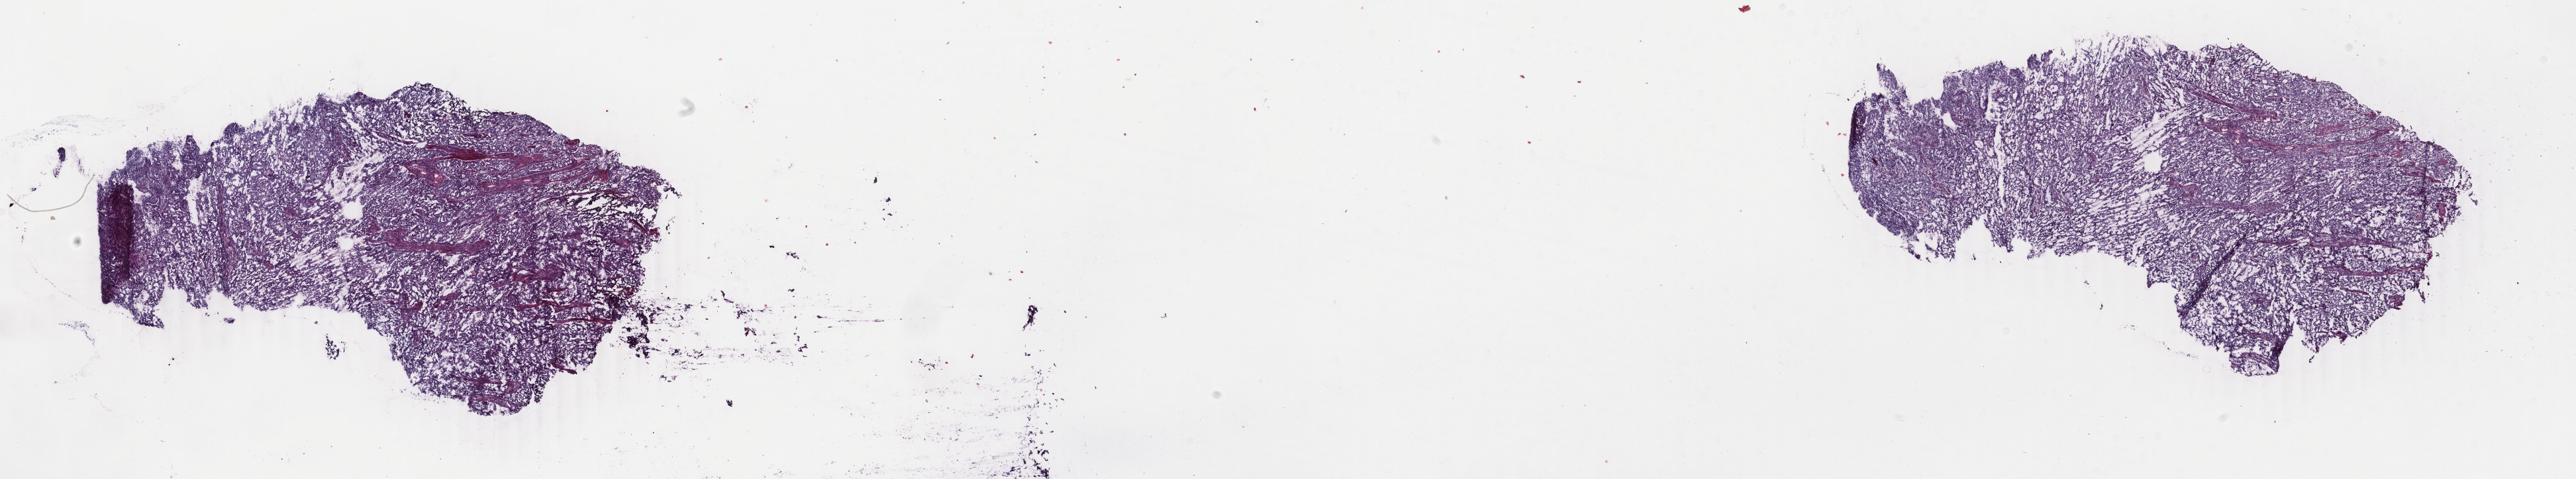
H&E whole-slide image, whole scanned area (about 30.9 x 5.7 mm, slide scanned at 40x) shown as a low-resolution overview; frozen section; primary tumour sample from the uterus. Patient: female, age at initial diagnosis 53 years. Histologic grade: G3 (poorly differentiated). Slide review estimates, as recorded: tumour cells 89%, tumour nuclei 85%, normal cells 0%, stromal cells 10%, necrosis 1%. Infiltration values recorded for this section: lymphocyte infiltration 7%, monocyte infiltration 0%, neutrophil infiltration 0%.
FIGO stage: IIIC1. Diagnosis: Endometrioid adenocarcinoma, NOS (endometrium).